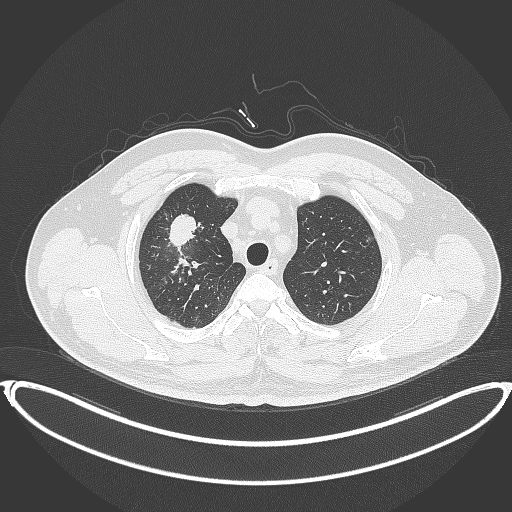
Chest CT, one axial slice. Position 314 of 399 along the scan axis. Lung window (W 1500 / L -600 HU). 1 mm slice thickness. 512 × 512 image matrix. Male patient, age 53 years. From the clinical record (not read from this slice): clinical TNM (as recorded): T2a N0 M0.
Annotated regions visible in this slice (bounding box drawn by a radiologist):
- lung tumour (recorded histology: adenocarcinoma): box from (x=166, y=211) to (x=200, y=253) px